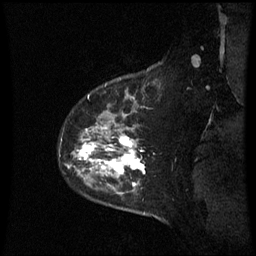
Breast MRI (dynamic contrast-enhanced), one sagittal slice. Position 50 of 60 along the scan axis. Dynamic contrast-enhanced series, image 2 of 3 at this slice position (ordered by acquisition). 1.5 T. TE 4.2 ms, TR 8.9 ms. 2.3 mm slice thickness. 256 × 256 image matrix, field of view 210 × 210 mm. Female patient, age 43 years. Case-level facts recorded for this patient, not image findings: setting: breast cancer imaged before/during neoadjuvant chemotherapy; receptor status: HER2-positive.
Outlined on this slice (semi-automatically segmented with operator editing):
- analysis volume of interest (the breast-tissue region the enhancement analysis was run in; not a lesion): bounding box (x1, y1, x2, y2) in pixels: (60, 80, 156, 195)
- tumour enhancement mask (voxels above the 70 % enhancement threshold inside the analysis volume of interest): (80, 129, 146, 187)